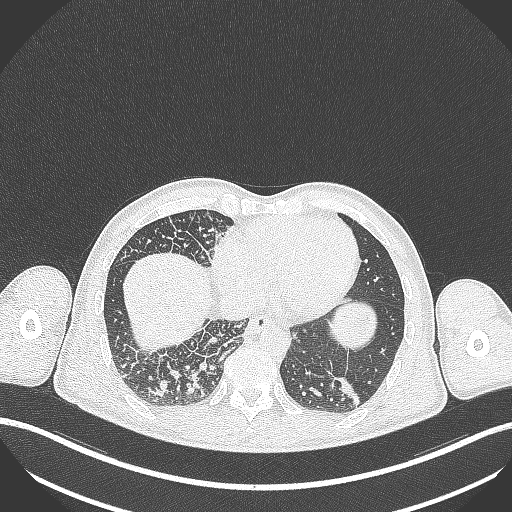
Chest CT, one axial slice; 120 kVp; lung window (W 1500 / L -600 HU); 512 × 512 image matrix, field of view 400 × 400 mm. Patient: male, 49 years. From the clinical record (not read from this slice): clinical TNM (as recorded): T2b N1 M0.
Outlined on this slice (rectangle marked by the reading radiologist):
- lung tumour (recorded histology: adenocarcinoma): box from (x=332, y=370) to (x=365, y=409) px